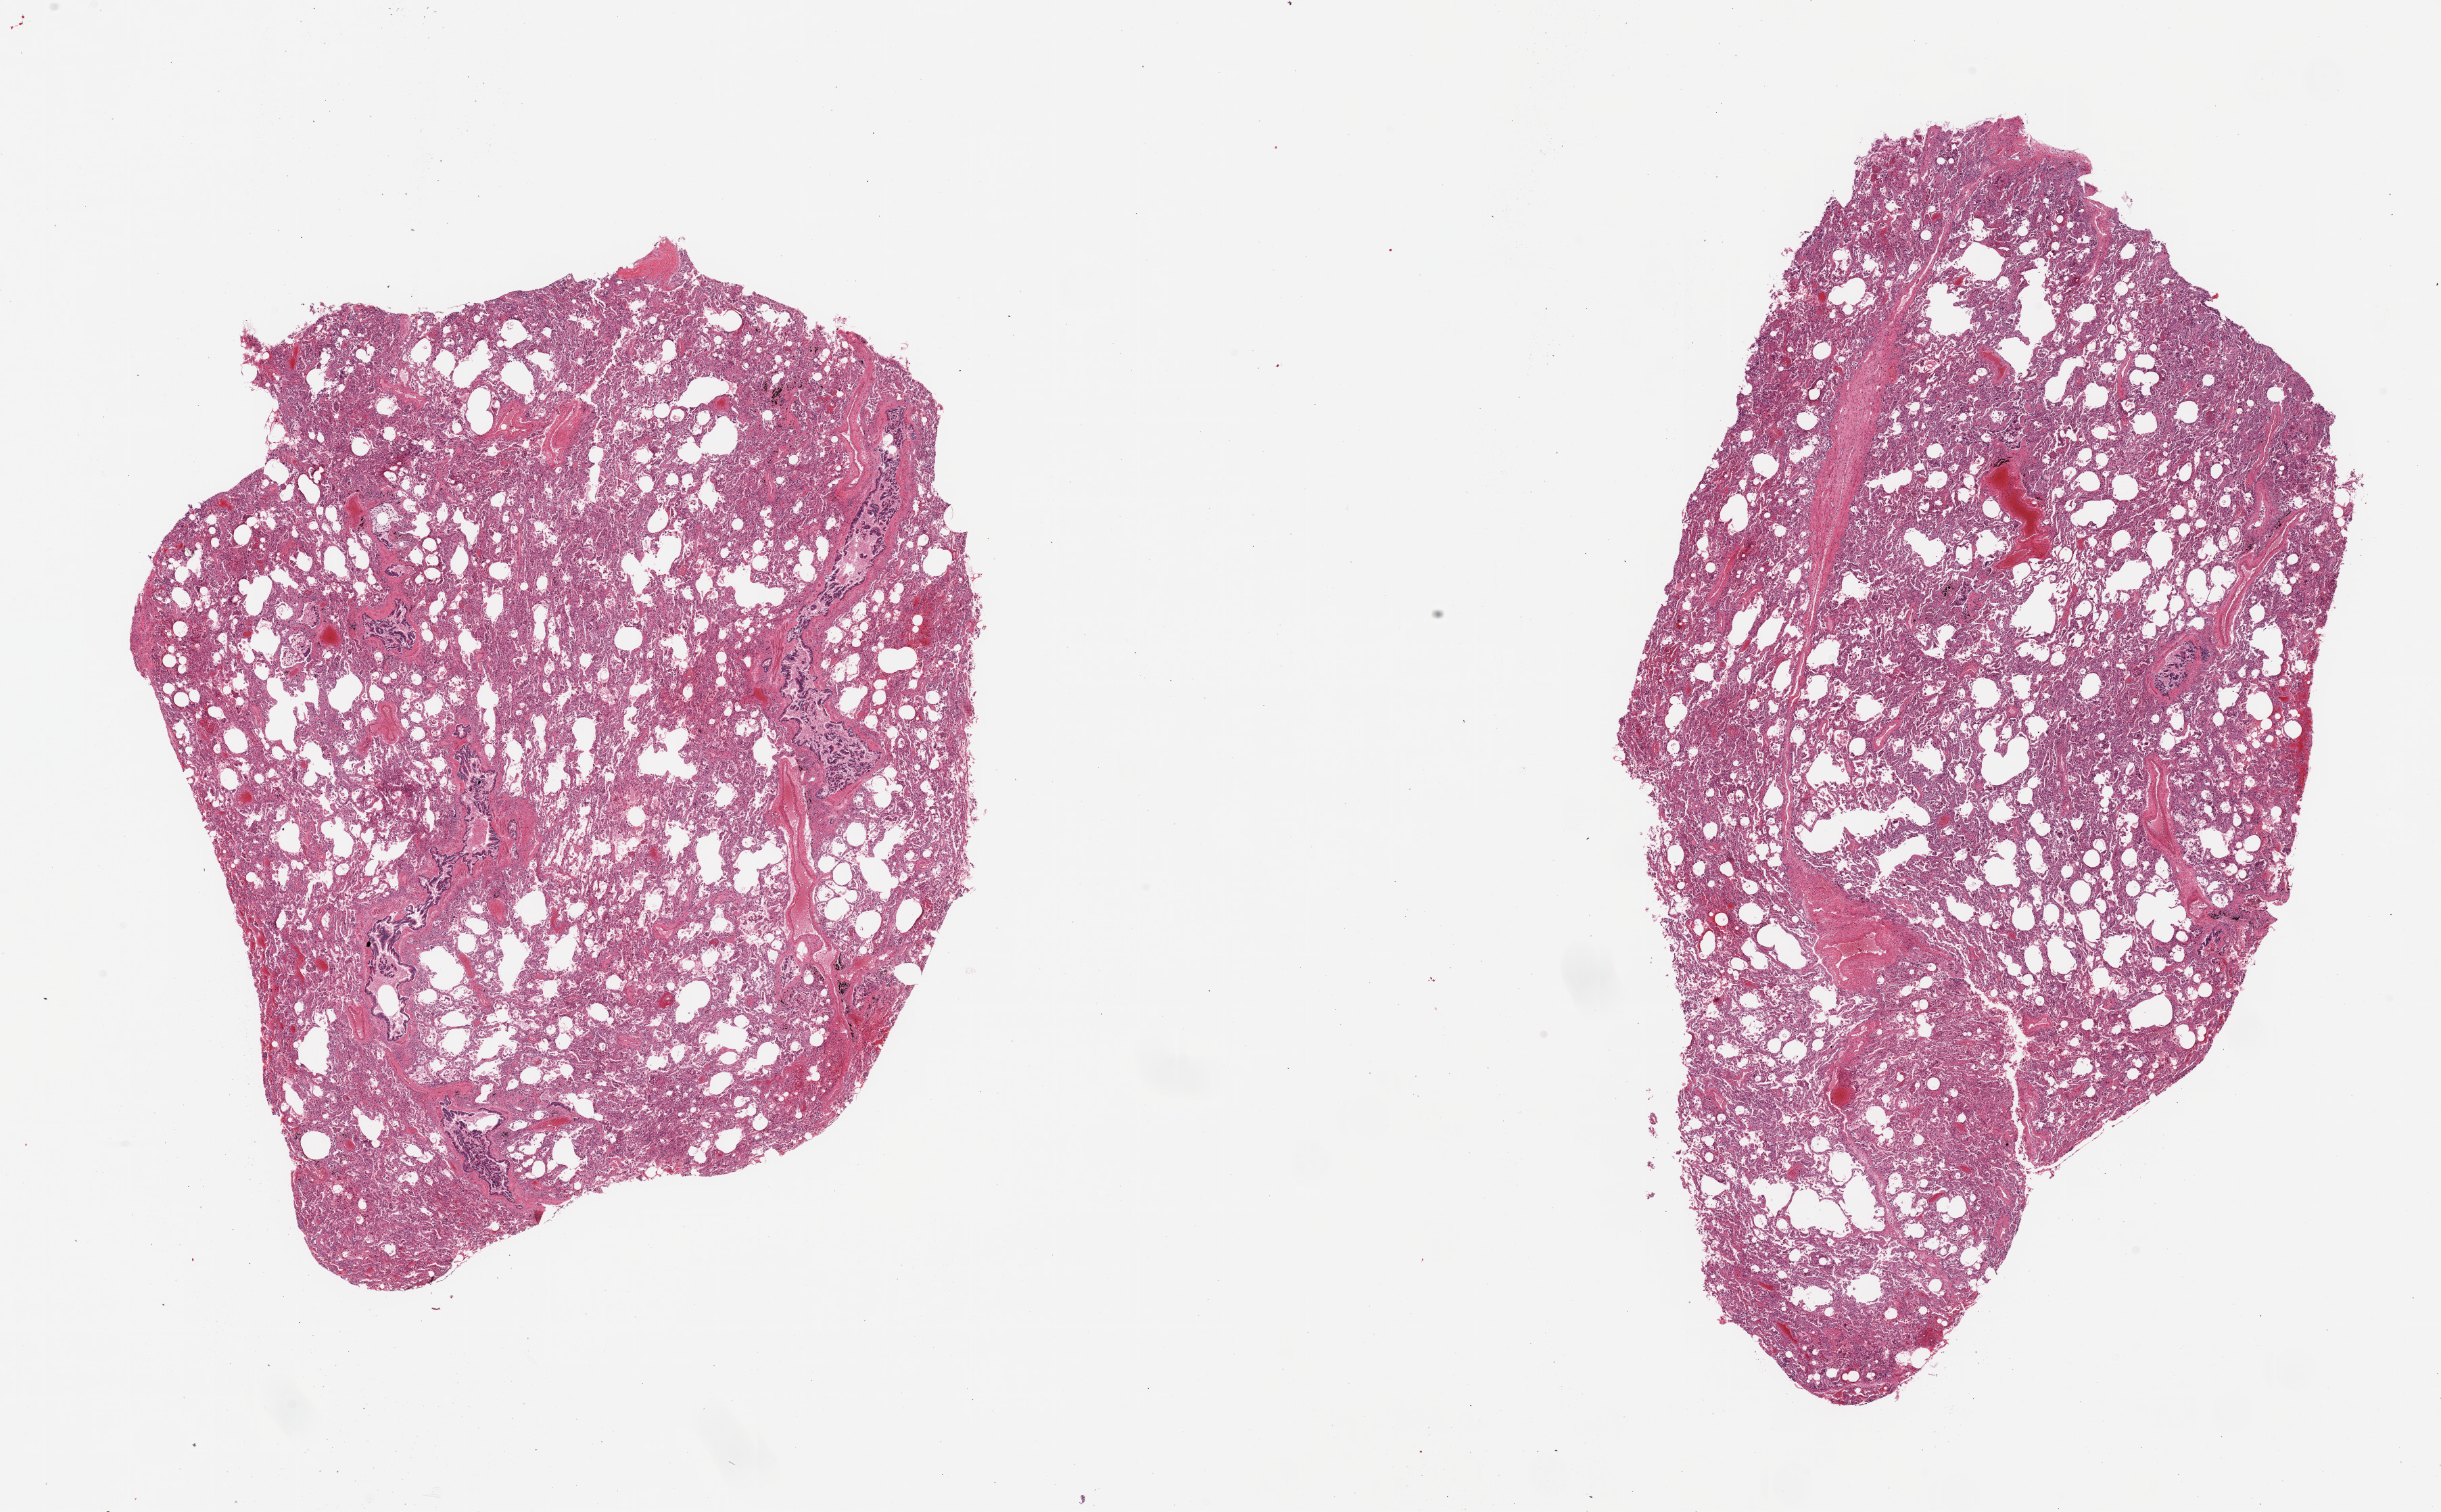
Whole-slide image, hematoxylin and eosin (H&E) stain, brightfield, whole scanned area (about 28.5 x 17.7 mm) shown as a low-resolution overview. PAXgene-fixed paraffin-embedded (PFPE) section. Section of lung (target tissue). Donor tissue sample. Donor sex: male.
- pathologist's review note for this sample: 2 pieces; patchy collapse, thickening of alveolar walls, numerous macrophages